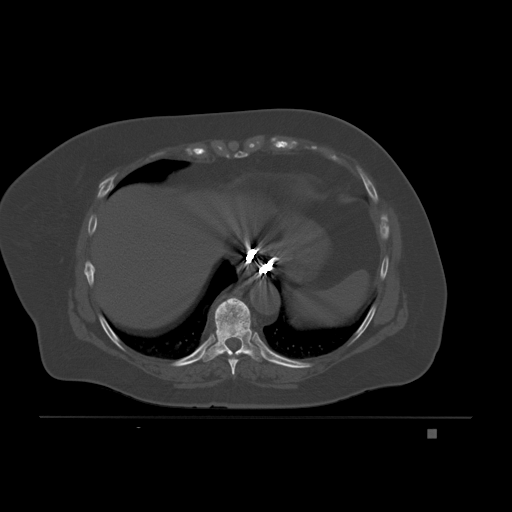
CT including the spine, one axial slice; slice 112 of 221 in the series (ordered by position); bone window (W 1800 / L 400 HU); 3 mm slice thickness; 512 × 512 image matrix, field of view 474 × 474 mm. Patient: female, 63 years. Case-level facts recorded for this patient, not image findings: primary cancer: breast.
Annotated regions visible in this slice (semi-automatically segmented with operator editing):
- T8 vertebra: bounding box <228,357,239,375> (left, top, right, bottom; pixels)
- T9 vertebra: <202,297,263,362>